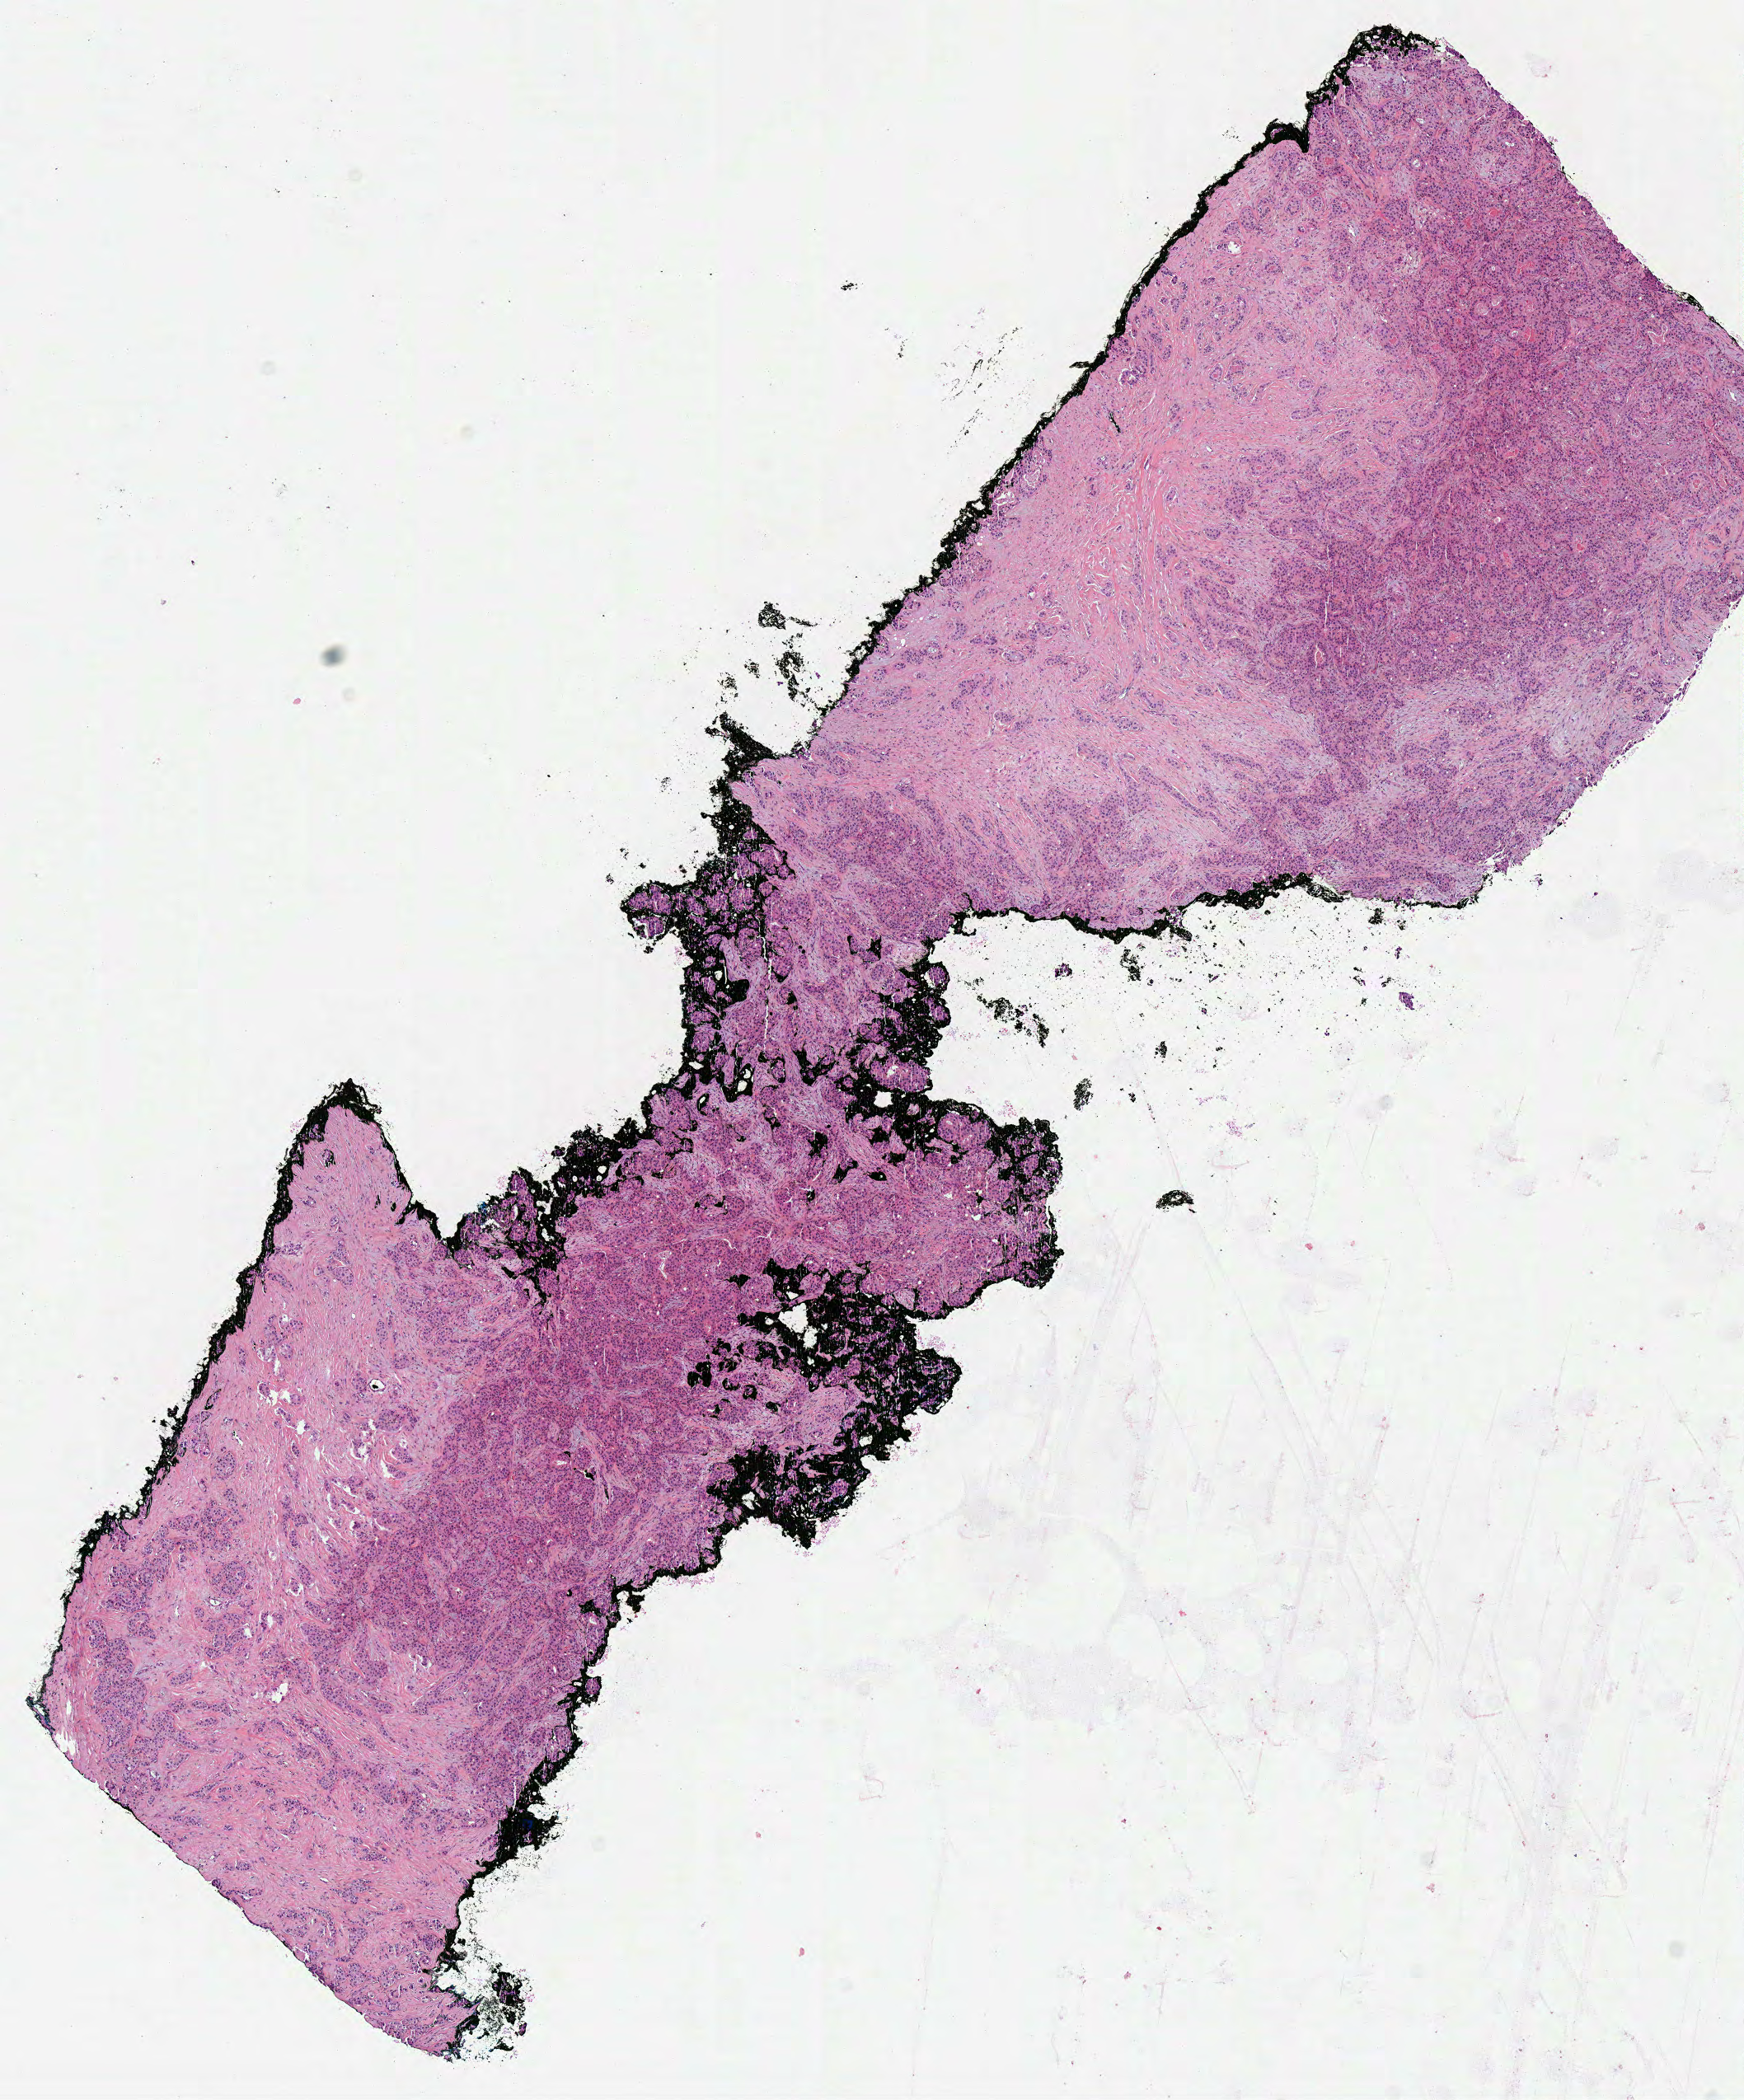
Digitized H&E tissue section (whole slide), whole scanned area (about 8.3 x 10.0 mm, acquisition: 40x scan) shown as a low-resolution overview. Formalin-fixed paraffin-embedded (FFPE) diagnostic section. Primary tumour sample from the breast. Patient sex: female.
Diagnosis: Infiltrating duct carcinoma, NOS. AJCC pathologic stage: IIA.